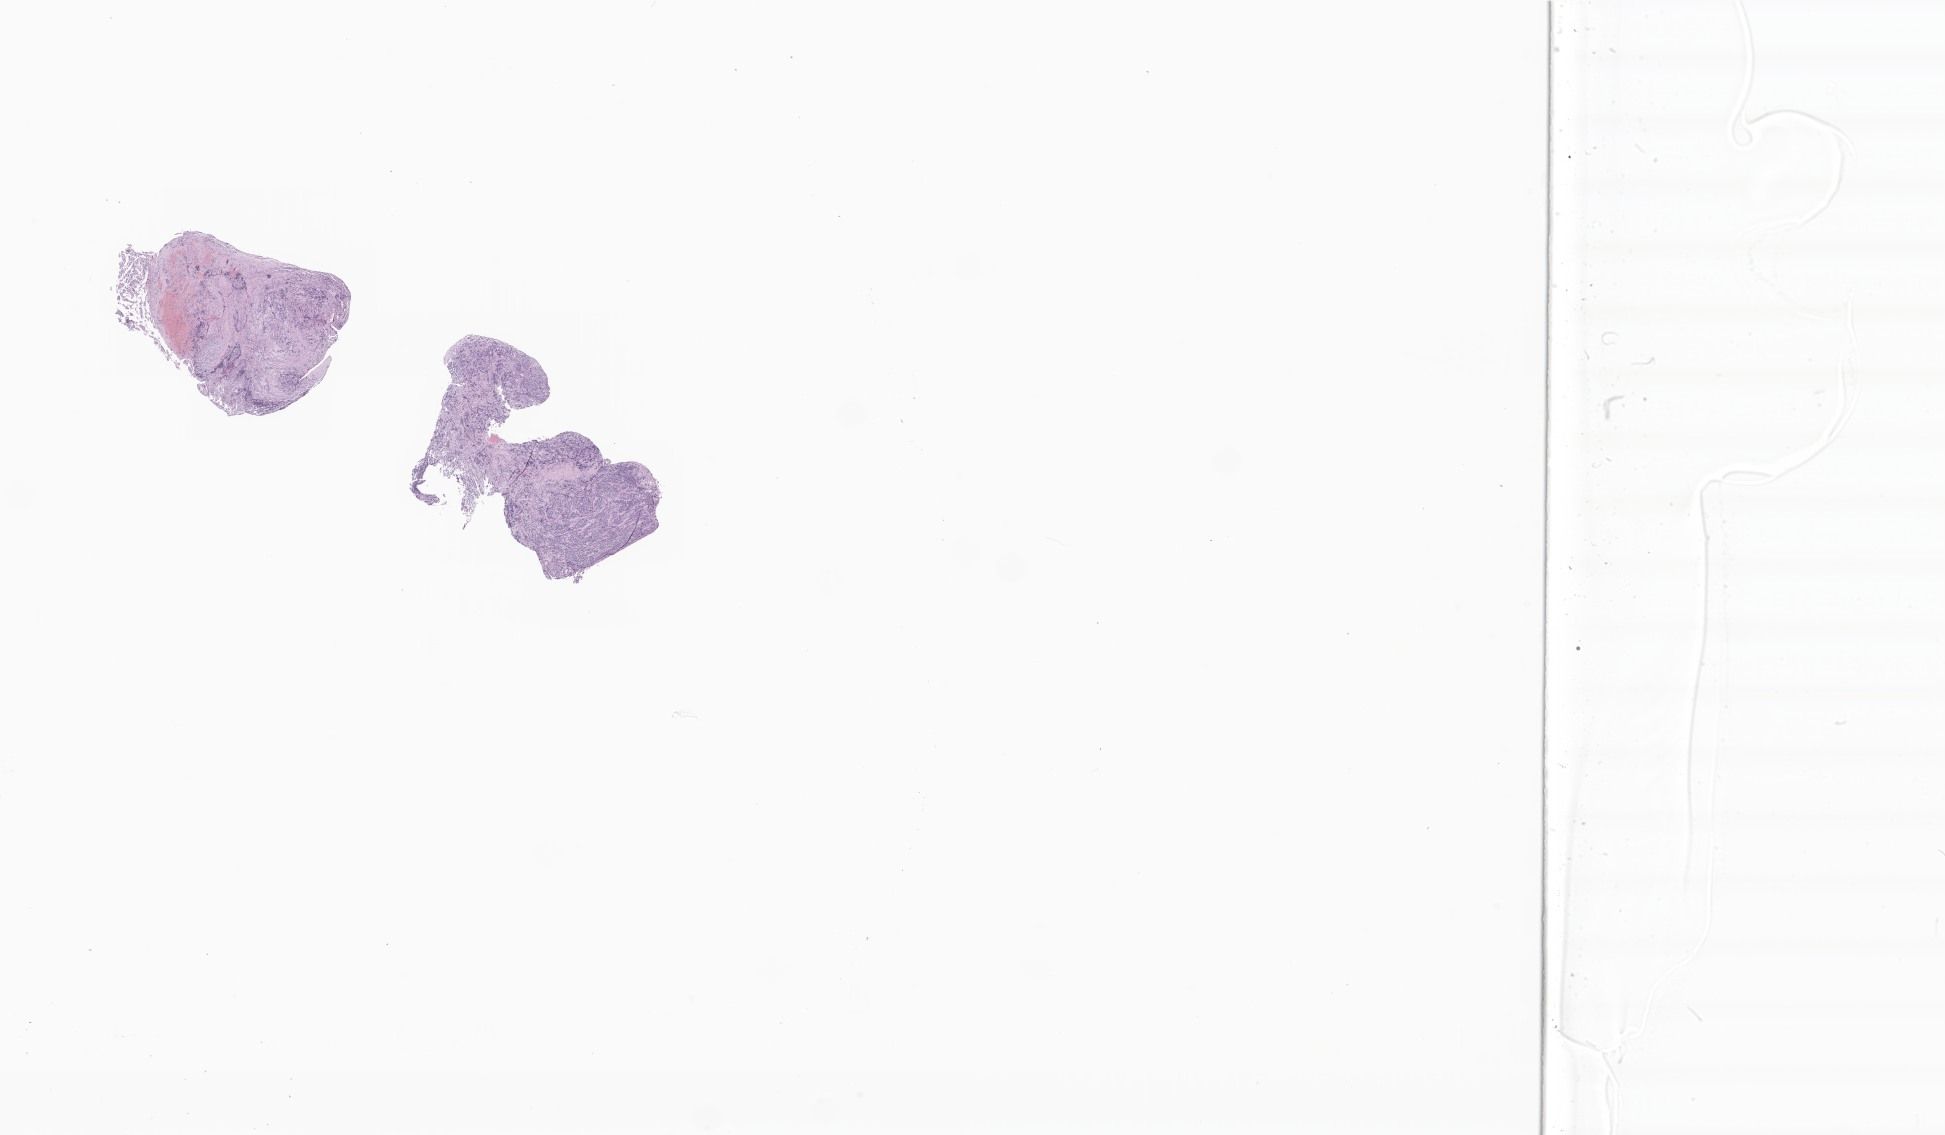
Digitized hematoxylin and eosin (H&E)-stained section of tumor tissue from the abdomen, a low-resolution overview of the entire scanned area, about 32.8 x 19.1 mm, formalin-fixed paraffin-embedded section. Female patient, age 111 days.
Diagnosis: Neuroblastoma, NOS.